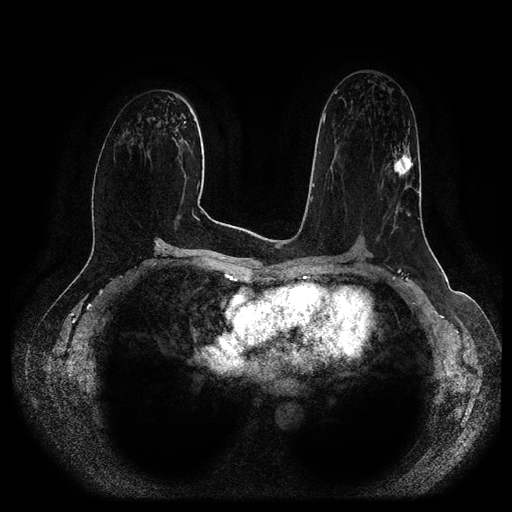
Breast MRI (dynamic contrast-enhanced, multi-phase), one axial slice; position 57 of 116 along the scan axis; dynamic contrast-enhanced series, time point 2 of 5 at this slice position (early post-contrast); 1.5 T; TE 2.6 ms, TR 5.2 ms; 512 × 512 image matrix, field of view 380 × 380 mm. Patient: female, 57 years.
Outlined on this slice (semi-automatically segmented with operator editing):
- breast lesion (labelled 'tumour' in the annotation; benign lesions carry a separate 'benign' label): box from (x=388, y=150) to (x=414, y=178) px